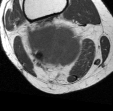
MRI of an extremity soft-tissue mass, one axial slice. Slice 33 of 45 in the series (ordered by position). MR volume resampled by the dataset authors to the PET/CT grid (not the native acquisition matrix). 3.27 mm slice thickness. 113 × 111 image matrix, field of view 110 × 108 mm. Female patient. Case-level facts recorded for this patient, not image findings: histological type: liposarcoma; site of the primary tumour: right thigh.
Annotated regions visible in this slice (expert contour drawn on MRI and transferred to this co-registered scan by the dataset authors):
- gross tumour volume (mass): bounding box (x1, y1, x2, y2) in pixels: (24, 21, 84, 70)